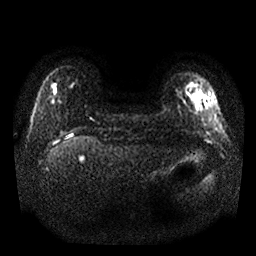
Breast MRI, one axial slice; position 2 of 25 along the scan axis; diffusion-weighted series; image 2 of 4 stored at this slice position (different b-values; order by instance number); 1.5 T; 4 mm slice thickness; 256 × 256 image matrix. Female patient.
Annotated regions visible in this slice (expert manual segmentation):
- tumour on diffusion-weighted imaging: bounding box <195,89,203,111> (left, top, right, bottom; pixels)